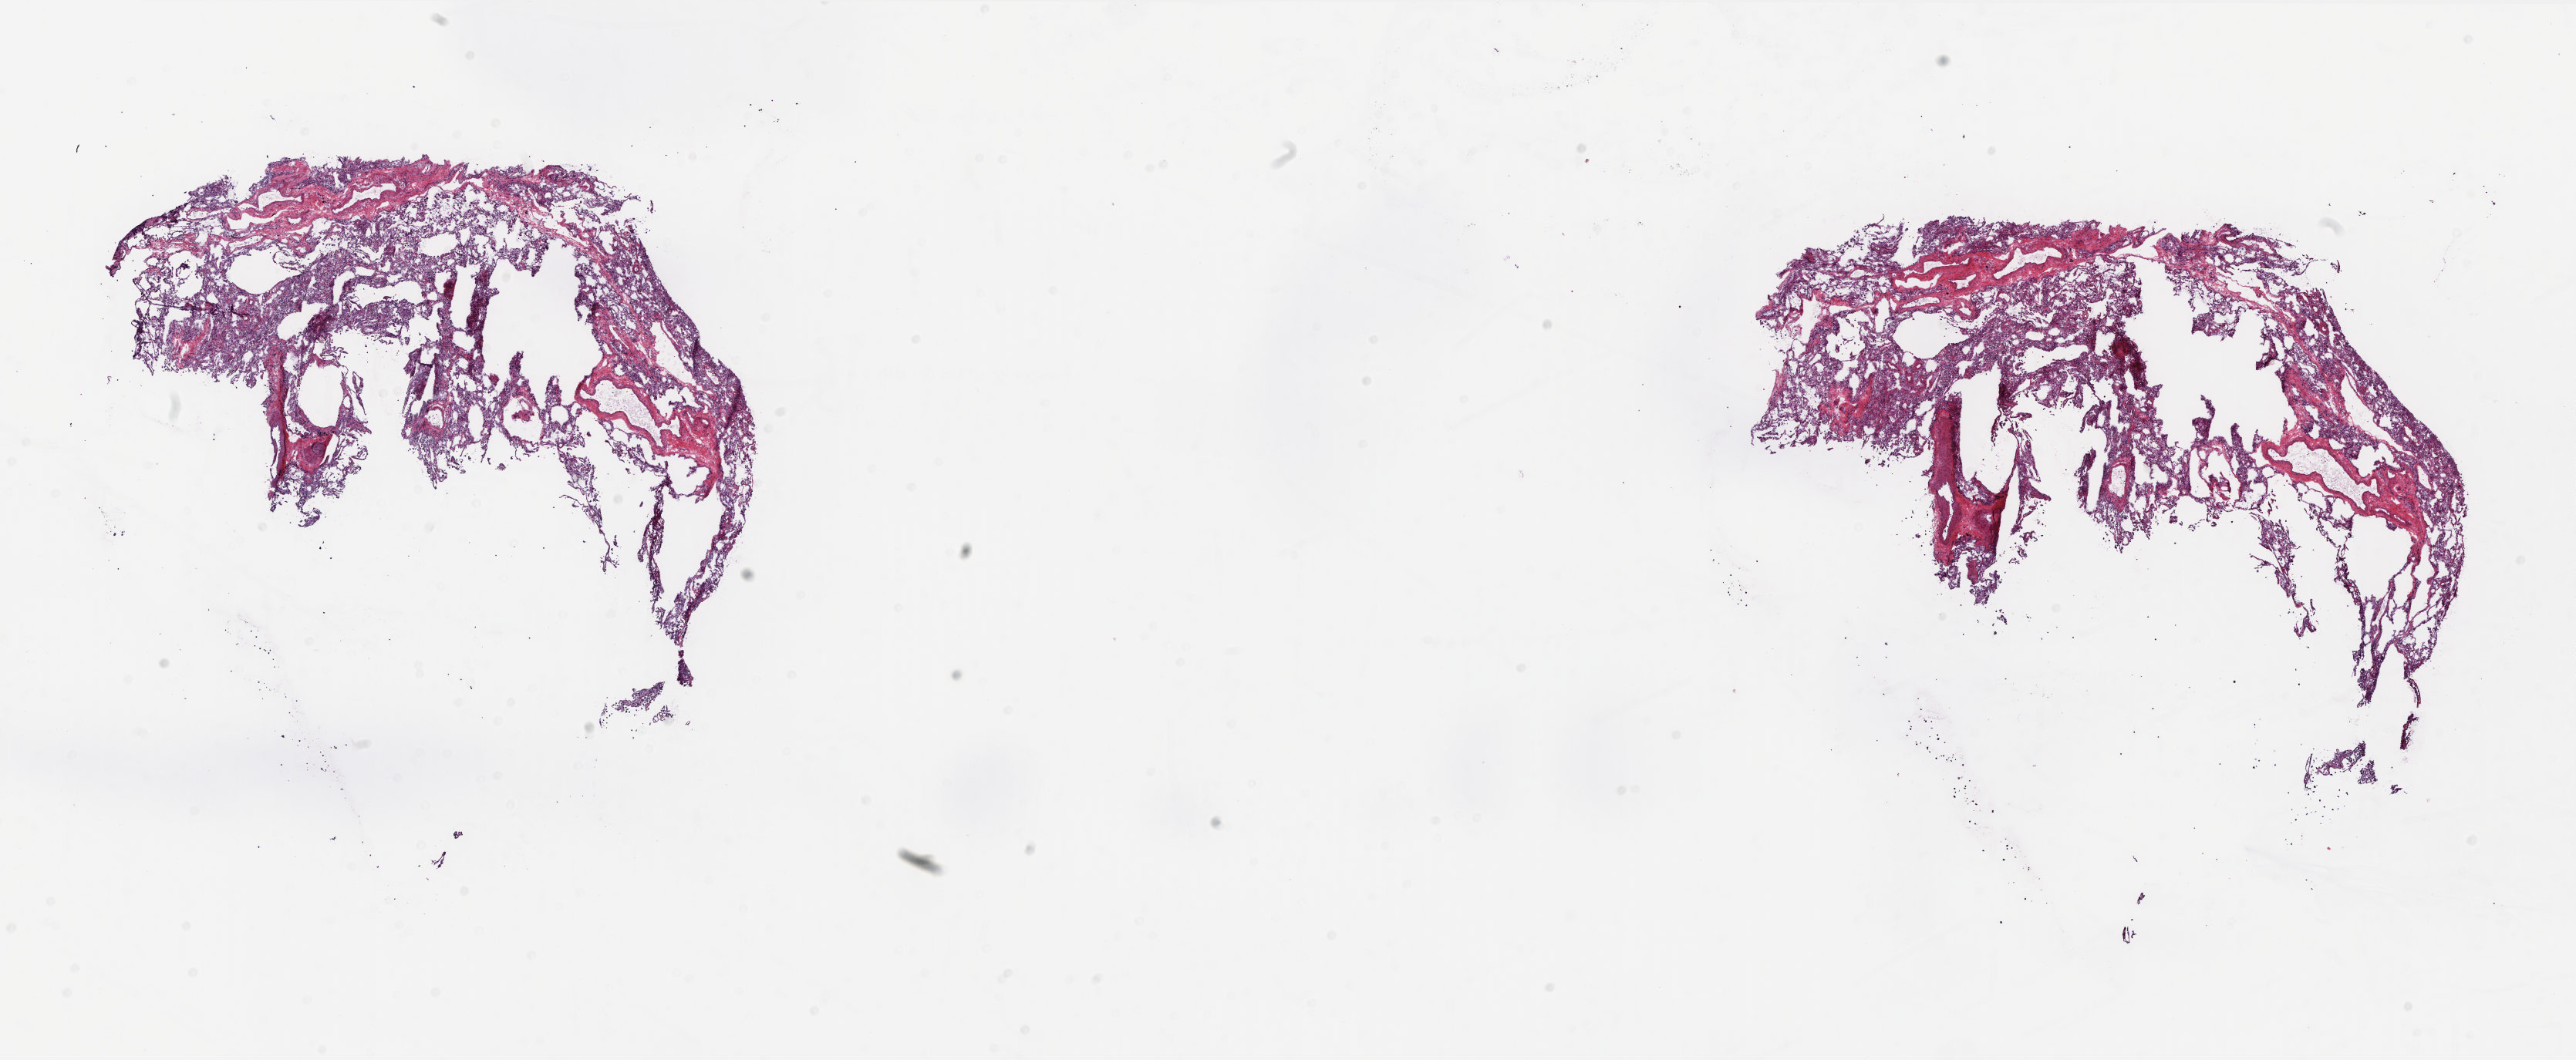
Digitized Hematoxylin and eosin (H&E) stained tissue section (whole slide), shown as a low-resolution overview of the whole scanned area (about 26.9 x 11.1 mm). Frozen section. Sample: solid tissue normal (non-tumour tissue), lung. Male patient; age at initial diagnosis 59 years. Composition of this section per pathologist review: tumour cells 0%, tumour nuclei 0%, normal cells 100%, stromal cells 0%, necrosis 0%. Inflammatory infiltration, as recorded: lymphocyte infiltration 20%, monocyte infiltration 20%, neutrophil infiltration 40%.
This section: solid tissue normal (non-tumour) sample from the same patient. Patient diagnosis: Adenocarcinoma, NOS.